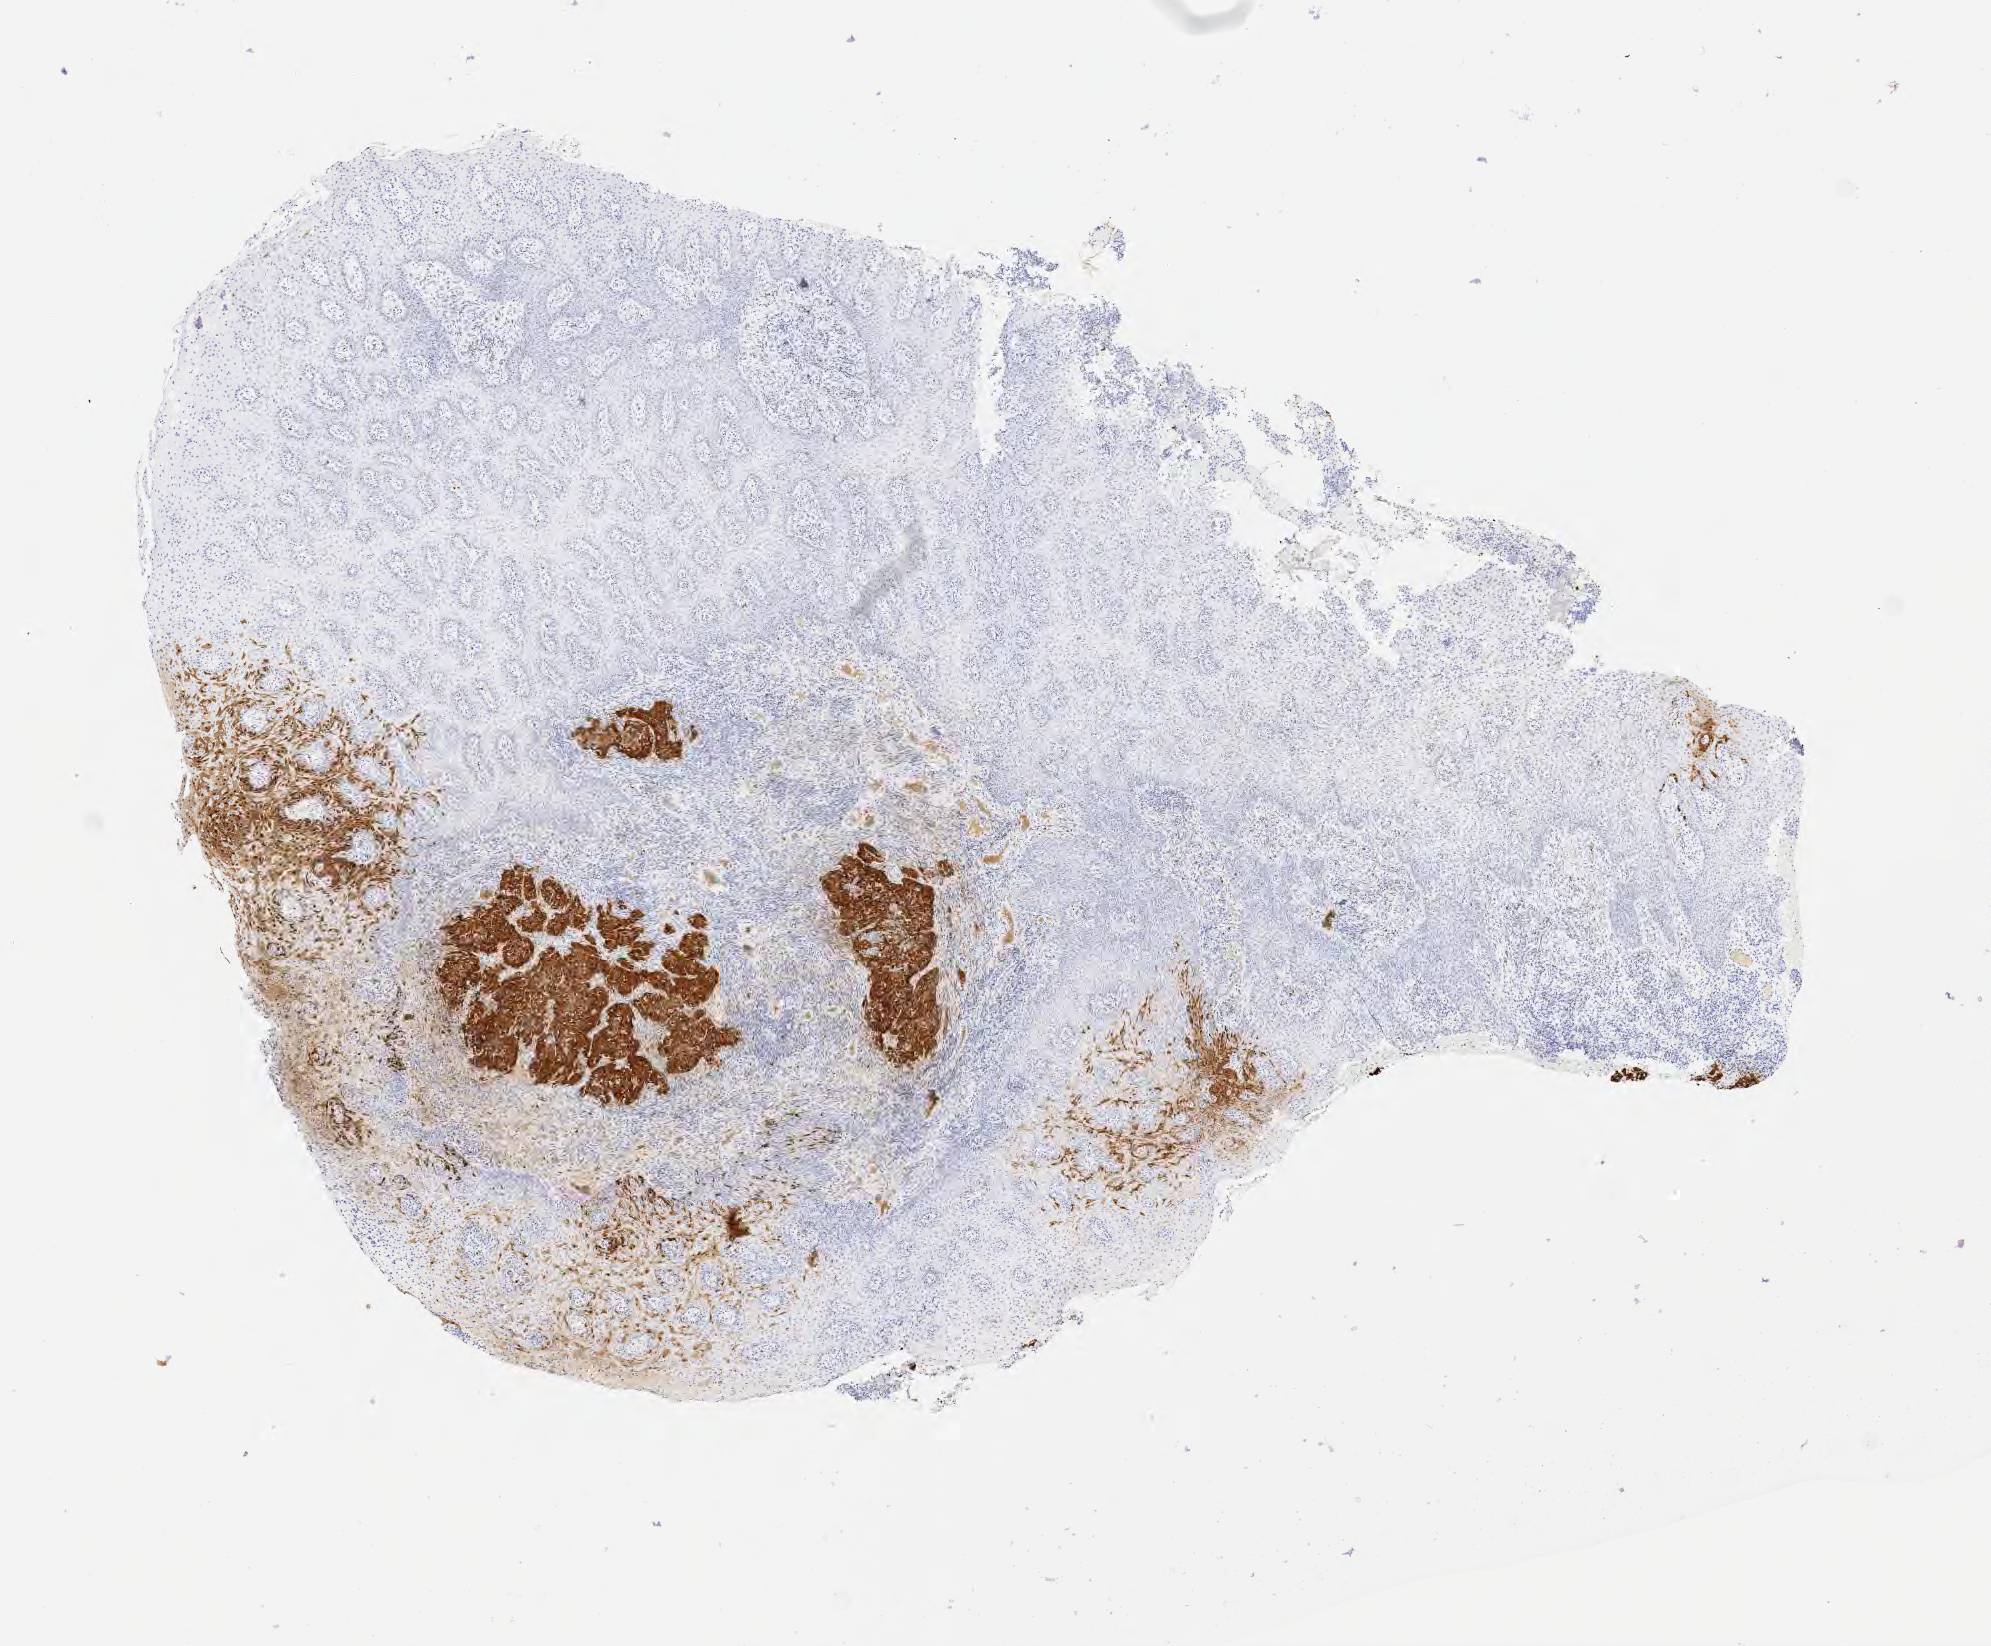
Immunohistochemistry (IHC) whole-slide image stained for p16 (p16INK4a), low-resolution overview of the scanned area, about 8.1 x 6.7 mm; specimen: tumor tissue; anatomic site: cervix. Patient female; 32 years old.
Diagnosis: Squamous cell carcinoma, large cell, nonkeratinizing, NOS.